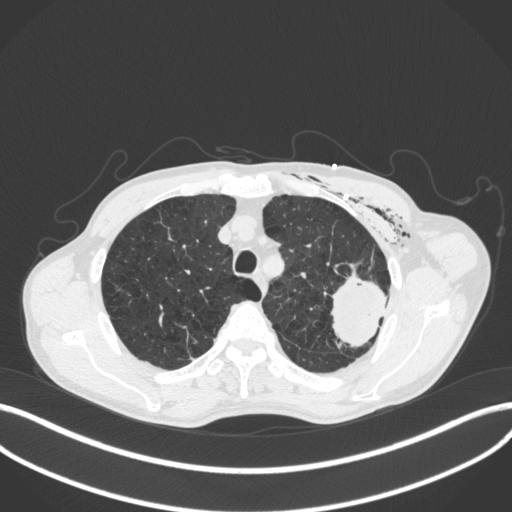
Chest CT, one axial slice; position 320 of 416 along the scan axis; 120 kVp; lung window (W 1500 / L -600 HU); 1 mm slice thickness; 512 × 512 image matrix, field of view 400 × 400 mm. Male patient, age 58 years. From the clinical record (not read from this slice): clinical TNM (as recorded): T3 N0 M0.
Outlined on this slice (rectangle marked by the reading radiologist):
- lung tumour (recorded histology: adenocarcinoma): box from (x=328, y=270) to (x=392, y=350) px